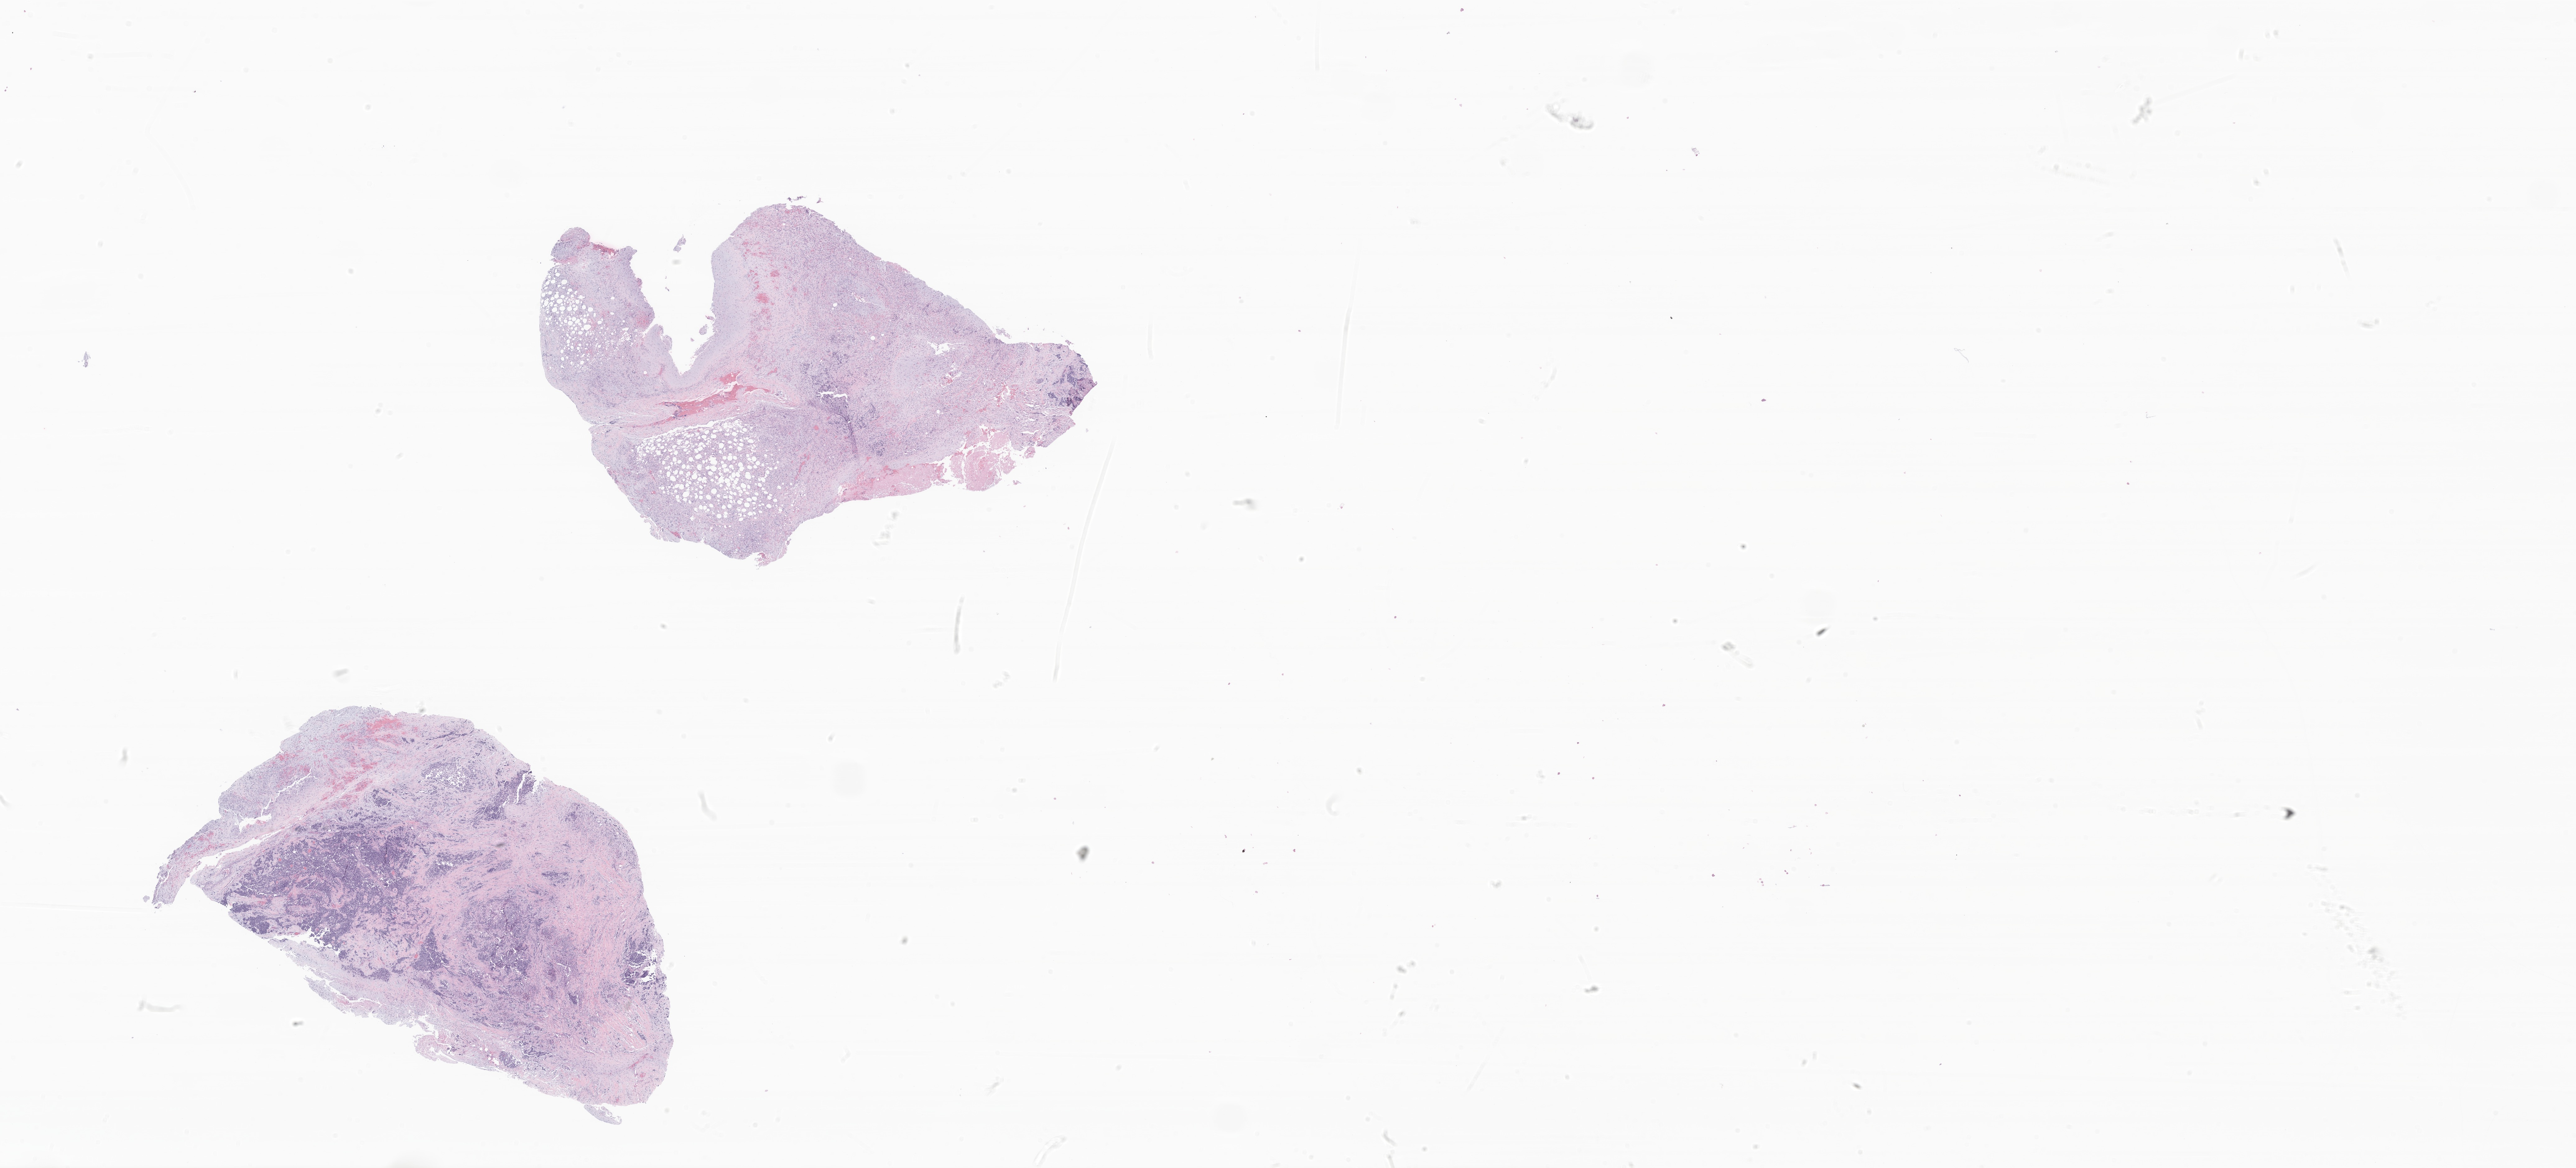
Whole-slide image, H&E stain of tumor tissue from the lower limb — a low-resolution overview of the entire scanned area, about 34.9 x 15.8 mm, formalin-fixed, paraffin-embedded (FFPE) tissue. Patient female; age 128 months (10 years 8 months).
Diagnosis: Rhabdomyosarcoma, NOS.